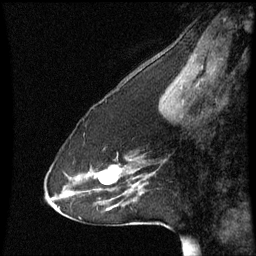
Breast MRI (dynamic contrast-enhanced), one sagittal slice. Slice 22 of 60 in the series (ordered by position). Dynamic contrast-enhanced series, image 2 of 3 at this slice position (ordered by acquisition). 1.5 T. TE 4.2 ms, TR 8.9 ms. 2.2 mm slice thickness. 256 × 256 image matrix, field of view 200 × 200 mm. Female patient, age 53 years. From the clinical record (not read from this slice): setting: breast cancer imaged before/during neoadjuvant chemotherapy; receptor status: HR-positive, HER2-negative.
Outlined on this slice (semi-automatically segmented with operator editing):
- analysis volume of interest (the breast-tissue region the enhancement analysis was run in; not a lesion): box from (x=44, y=120) to (x=167, y=223) px
- tumour enhancement mask (voxels above the 70 % enhancement threshold inside the analysis volume of interest): (x=100, y=180)–(x=103, y=183)